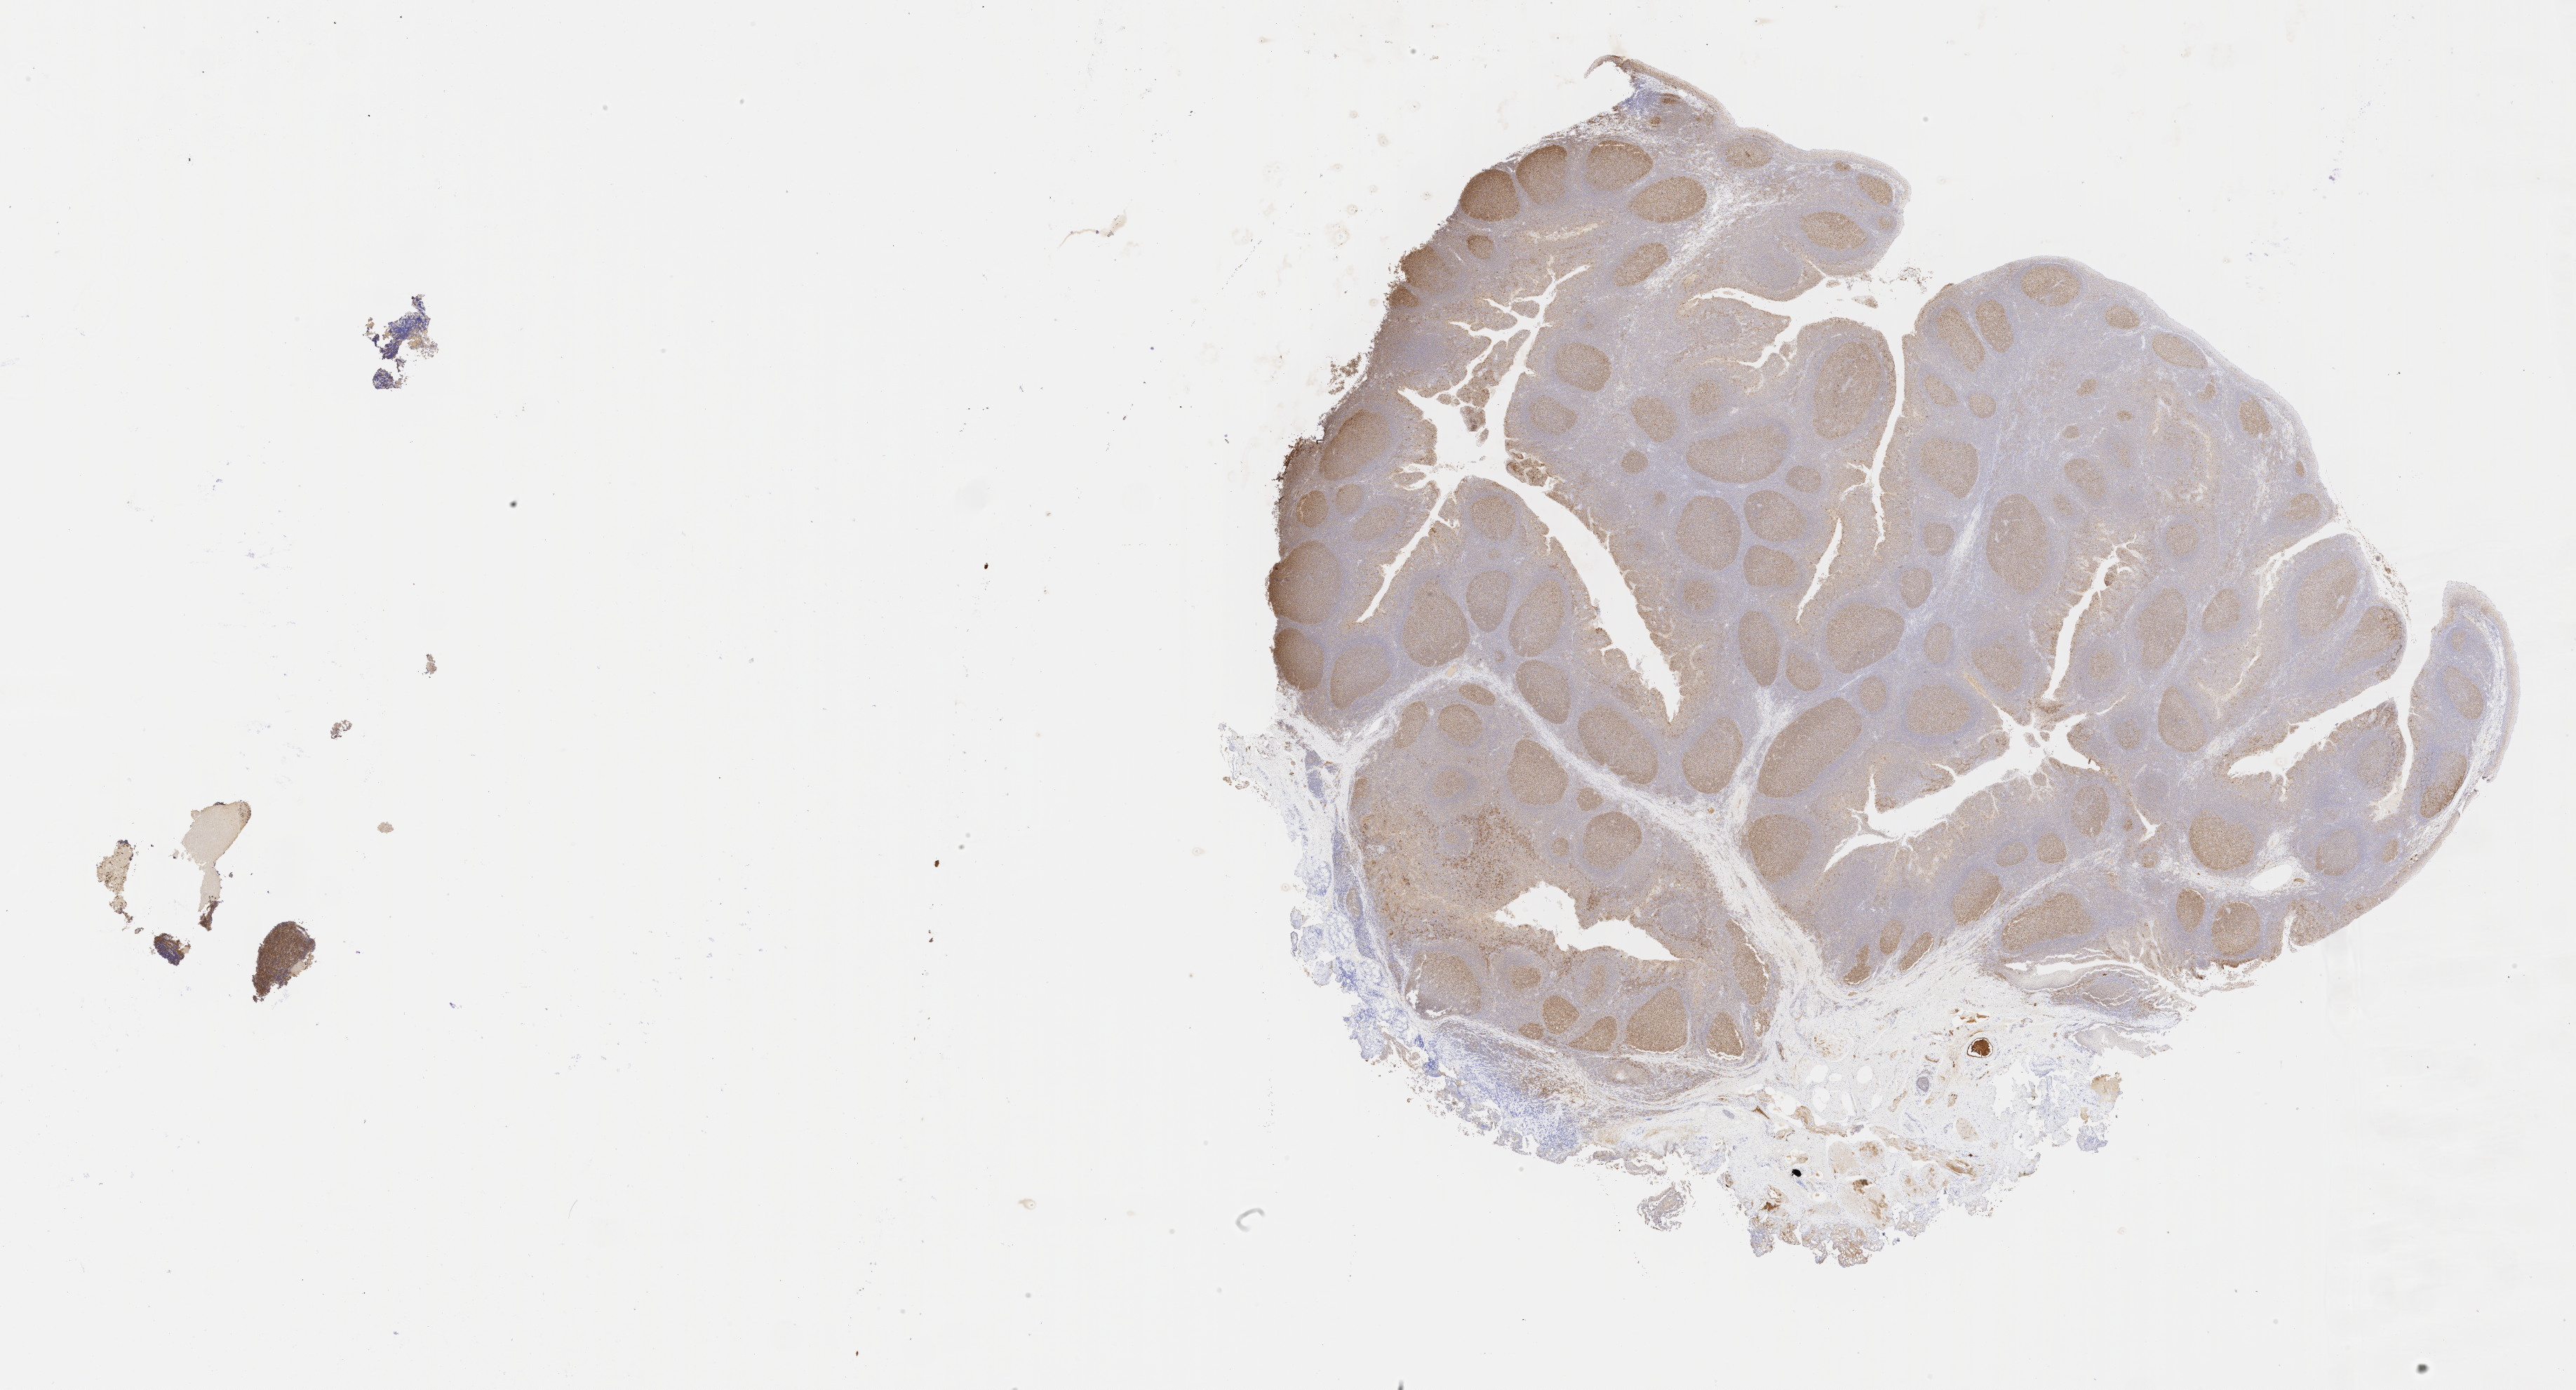
Immunohistochemistry (IHC) whole-slide image stained for BCL6 — shown as a low-resolution overview of the whole scanned area (about 29.7 x 16.0 mm); specimen: tumor tissue; site: abdominal lymph node. Male patient; age at initial diagnosis 5 years.
• histologic diagnosis: Diffuse large B-cell lymphoma, NOS